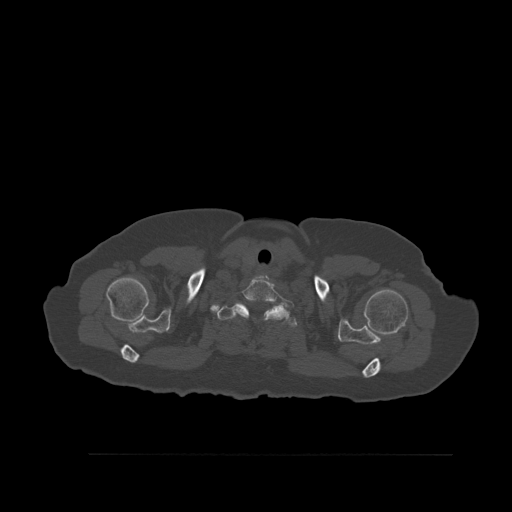
CT including the spine, one axial slice. Bone window (W 1800 / L 400 HU). 1.5 mm slice thickness. 512 × 512 image matrix, field of view 470 × 470 mm. Female patient, age 73 years. From the clinical record (not read from this slice): primary cancer: breast; vertebrae with lytic lesions (as recorded): L2.
Annotated regions visible in this slice (semi-automatic segmentation, software-assisted and operator-edited):
- T1 vertebra: bounding box <217,305,298,328> (left, top, right, bottom; pixels)